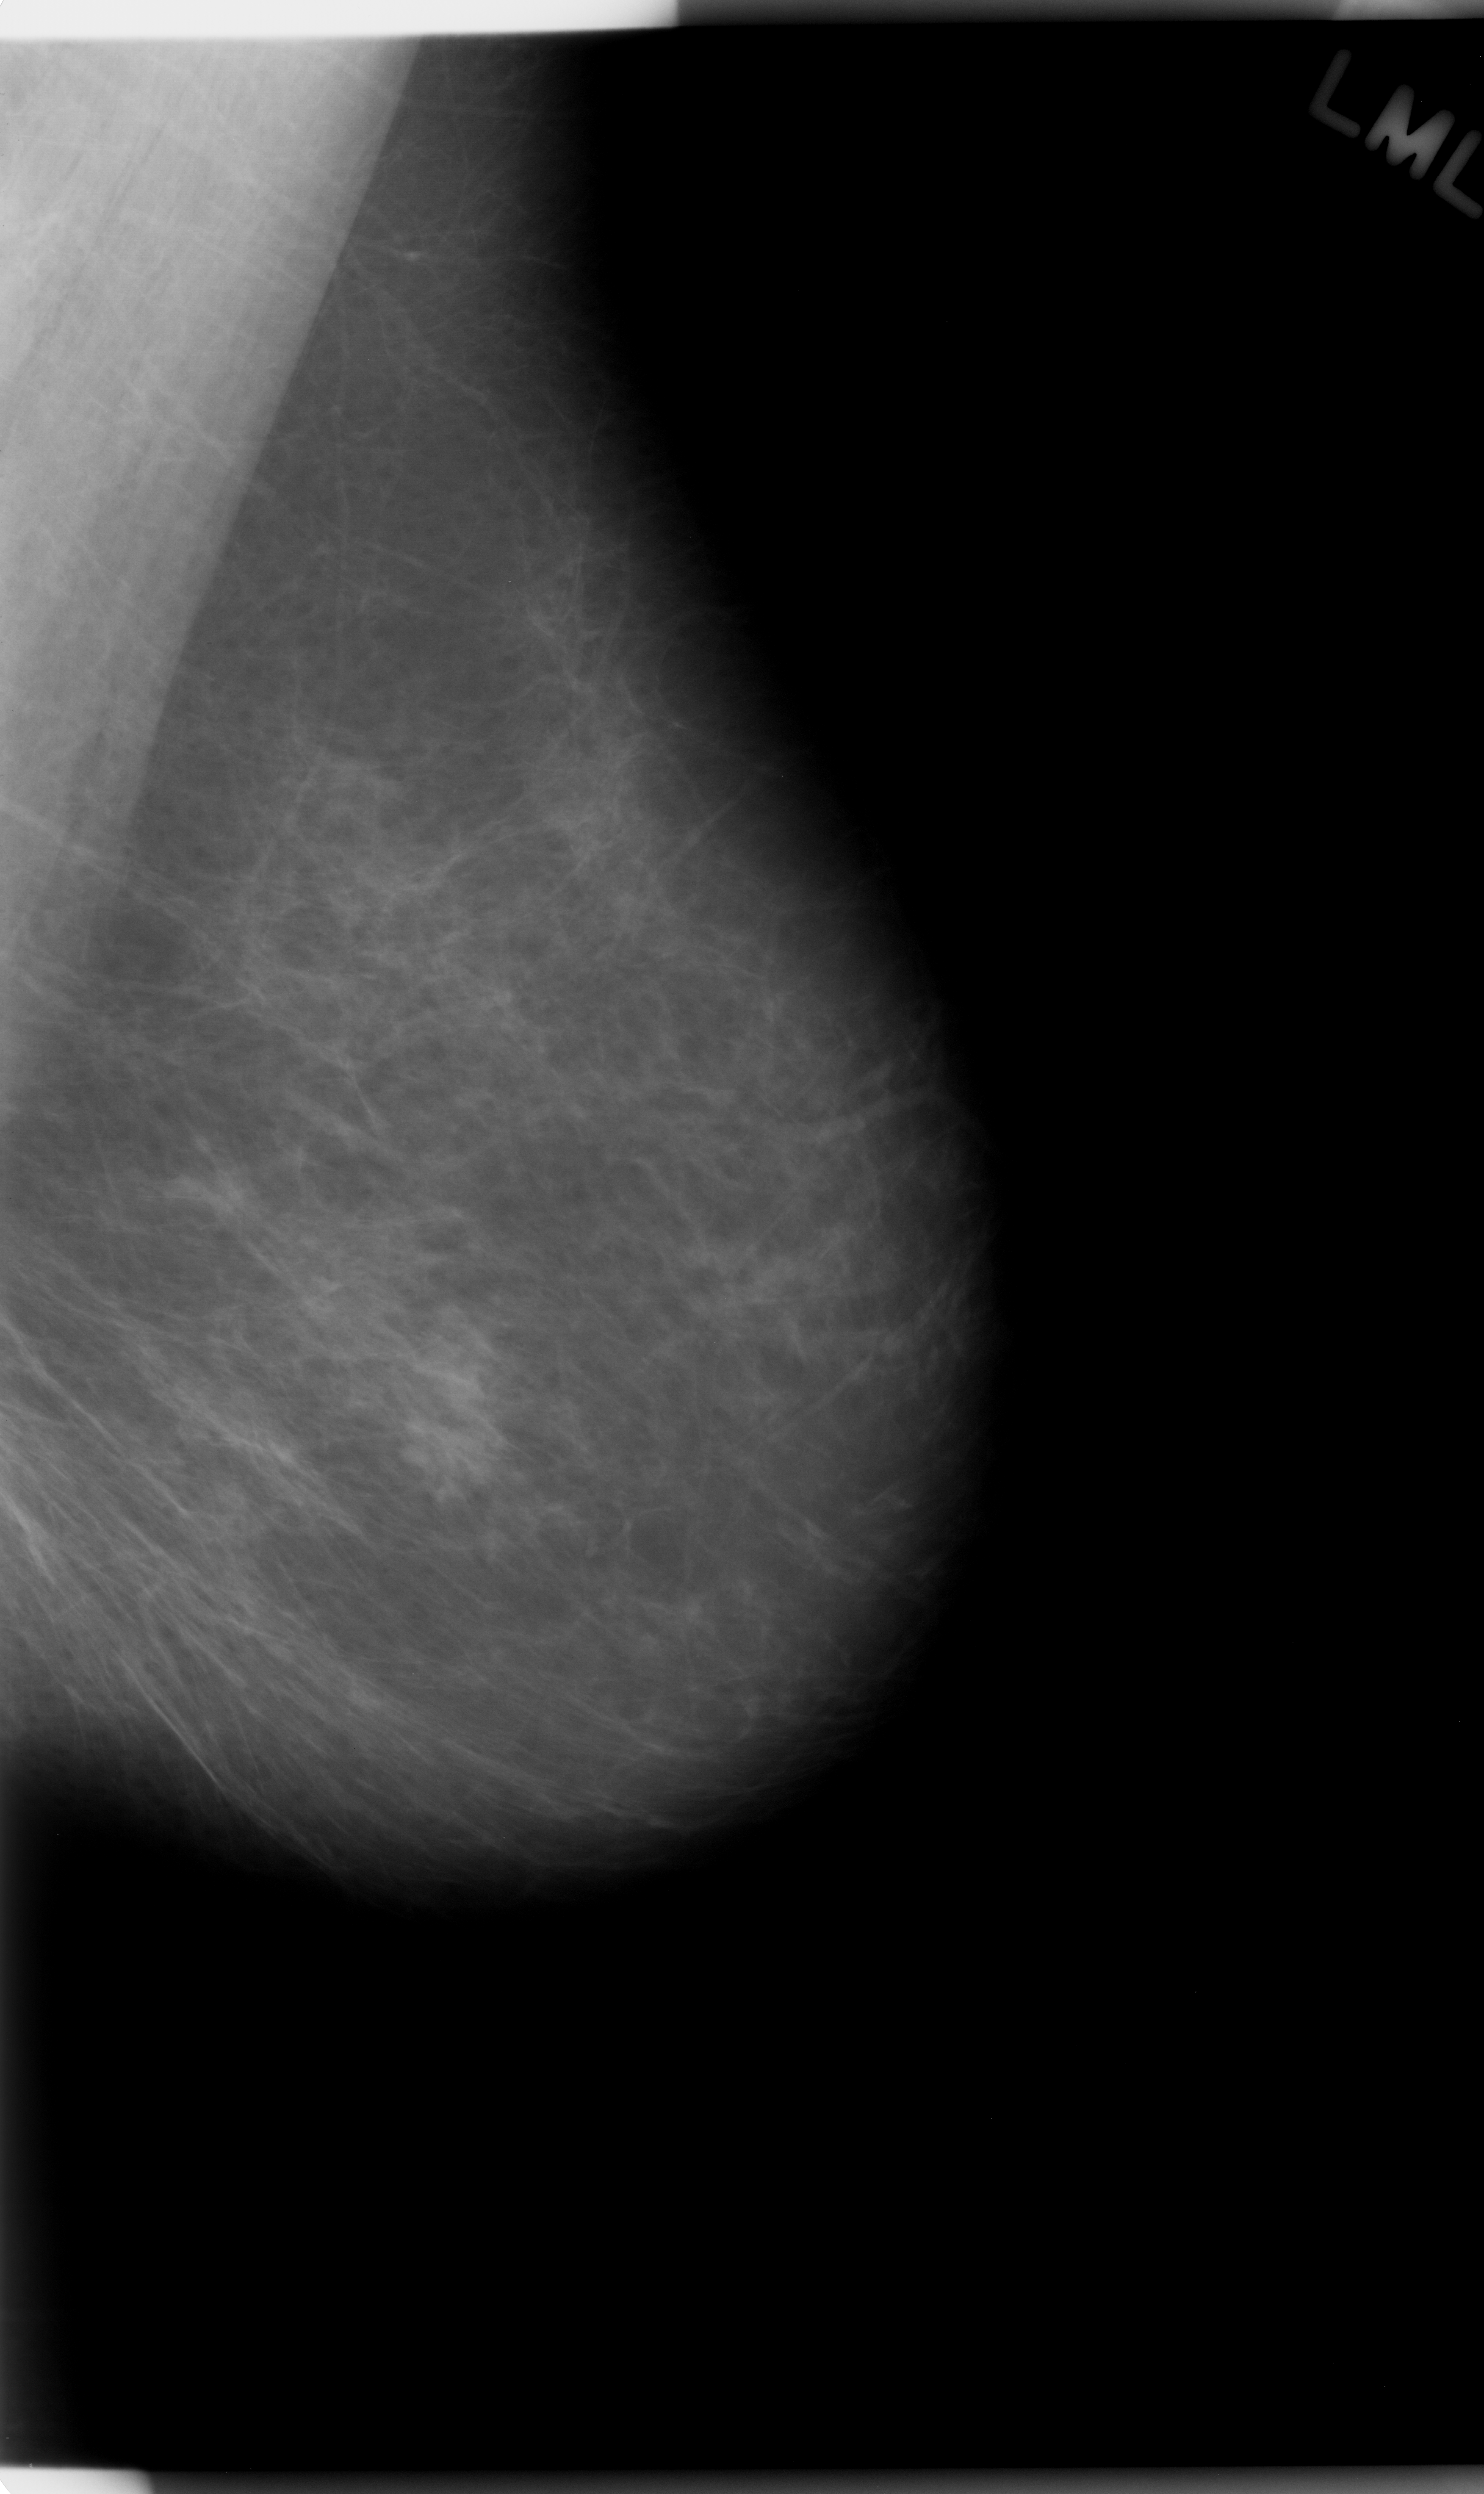
Scanned film-screen mammogram. Left breast. MLO view. BI-RADS breast density category 1 (scale 1–4). 1484 × 2494 image matrix.
Marked abnormalities (boxes around the expert regions of interest):
- mass, shape lobulated, margins ill defined; BI-RADS assessment category 4; subtlety rating 4 on a 1 (subtle) to 5 (obvious) scale; pathology (as recorded): malignant: bounding box (x1, y1, x2, y2) in pixels: (385, 1343, 515, 1505)